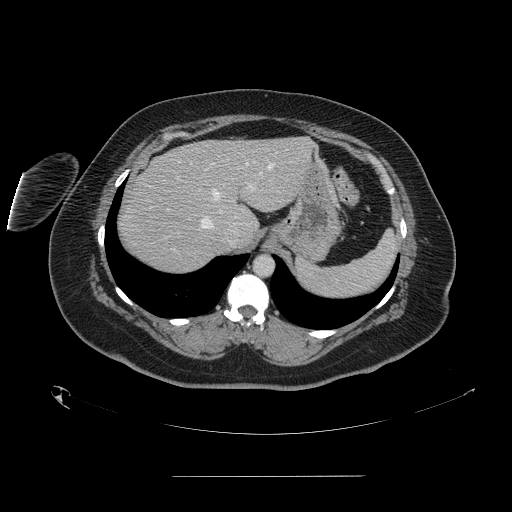
Contrast-enhanced abdominal CT, one axial slice; slice 119 of 164 in the series (ordered by position); 120 kVp; intravenous contrast given; soft-tissue window (W 400 / L 40 HU); 2.5 mm slice thickness; 512 × 512 image matrix, field of view 495 × 495 mm. Female patient, age 52 years. From the clinical record (not read from this slice): diagnosis: colorectal cancer liver metastases, imaged before liver resection; multiple liver metastases: yes; largest metastasis: 3.5 cm; disease in both lobes: no.
Annotated regions visible in this slice (expert manual segmentation):
- hepatic veins: box from (x=201, y=162) to (x=273, y=228) px
- liver: (x=118, y=138)–(x=312, y=273)
- planned liver remnant (the part of the liver to remain after resection): (x=169, y=137)–(x=313, y=226)
- portal vein (with intrahepatic branches): (x=176, y=177)–(x=253, y=212)